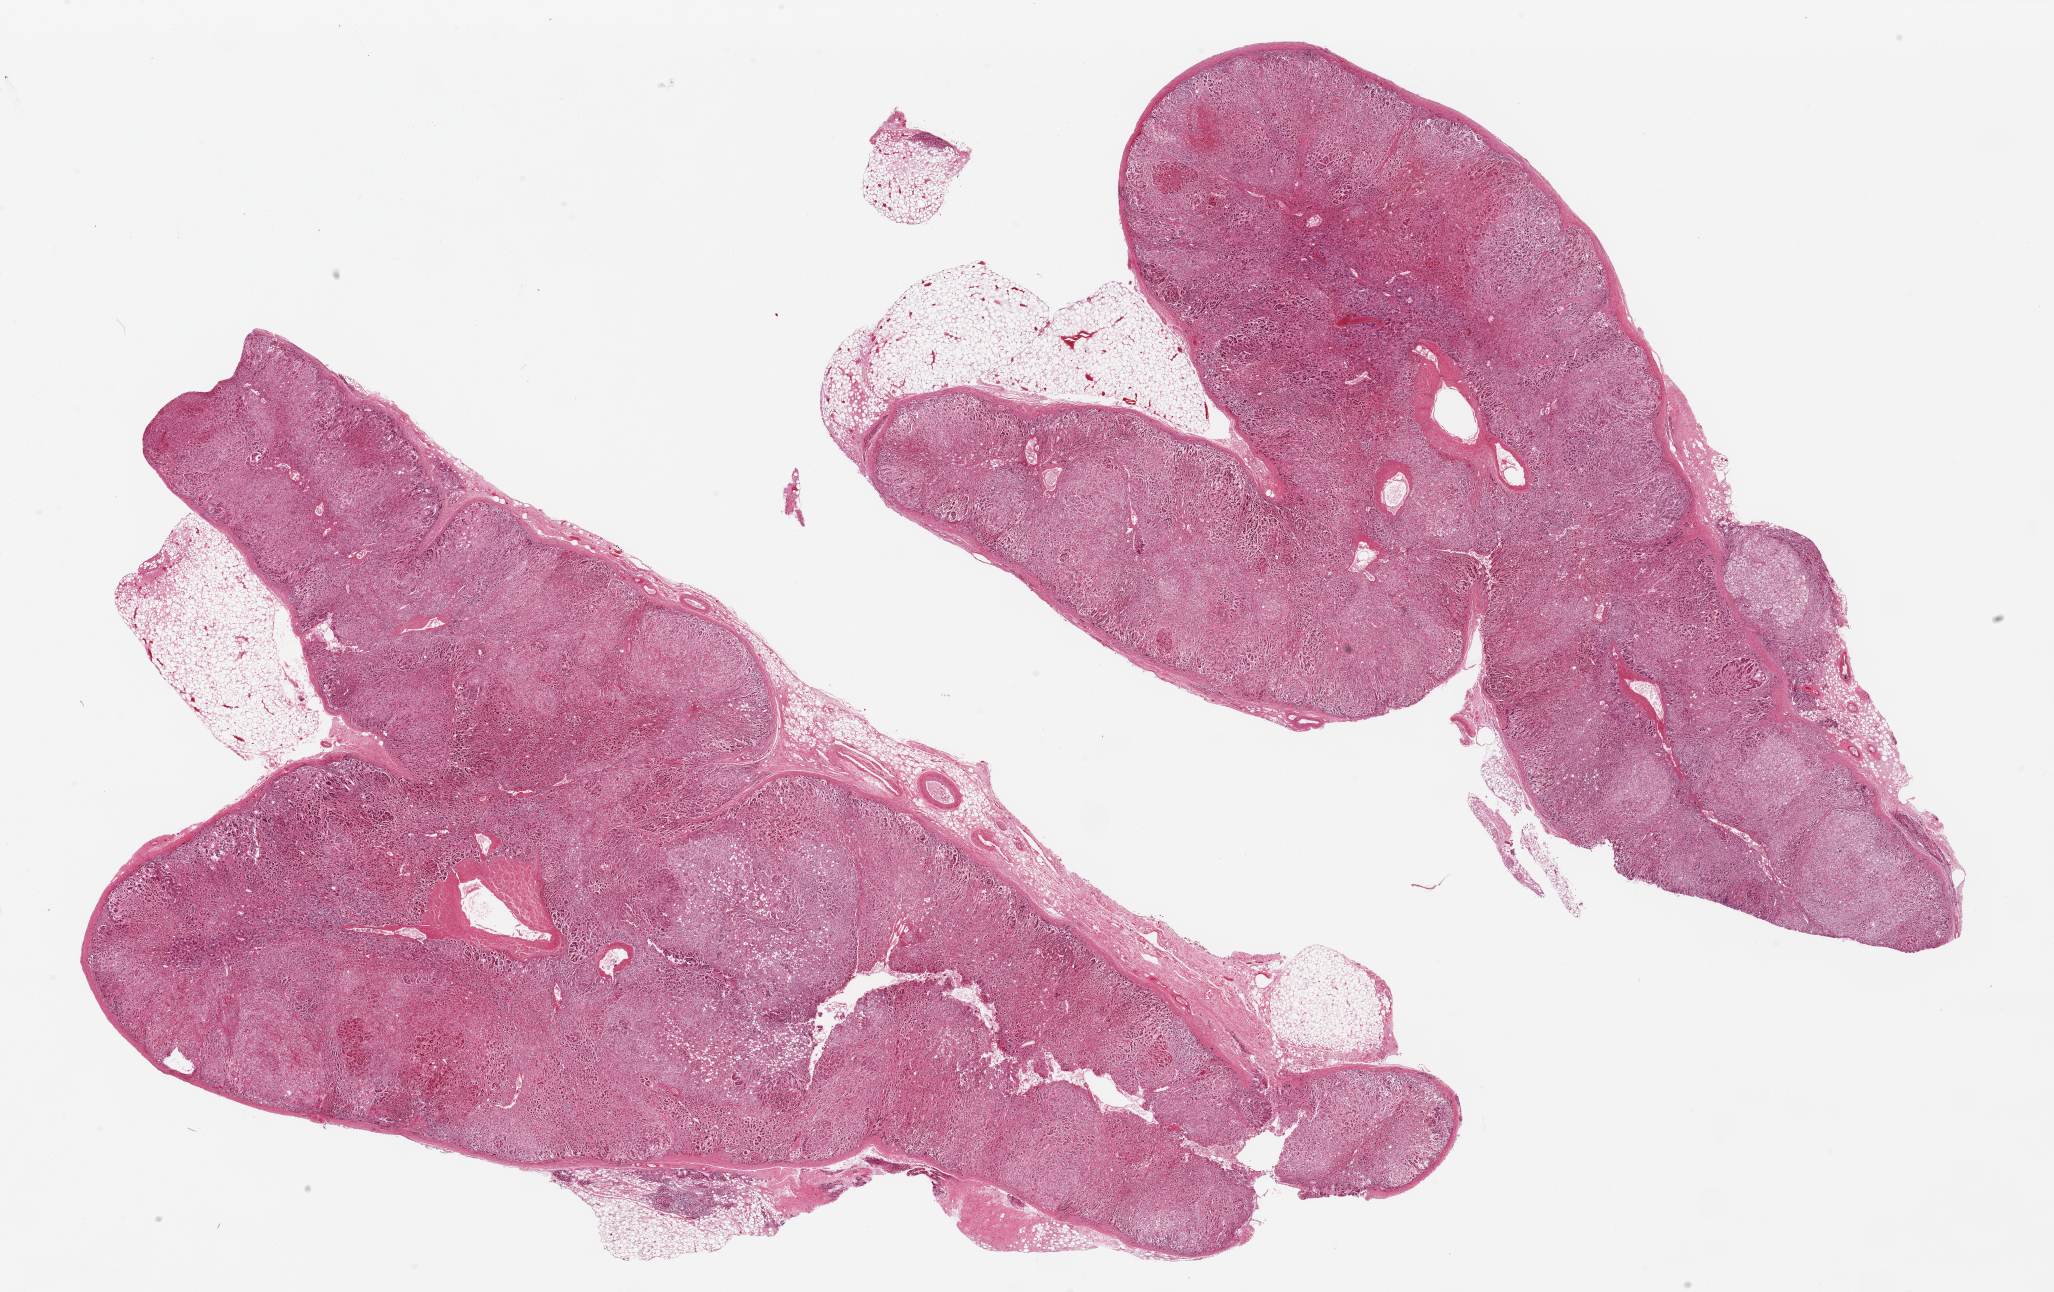
Whole-slide image, H&E stain, shown as a low-resolution overview of the whole scanned area (about 32.5 x 20.4 mm, slide scanned at 20x); PAXgene-fixed paraffin-embedded (PFPE) section; target tissue: adrenal gland; tissue donor sample.
* review note (as recorded): 2 ~20x10mm aliquots, all cortex, moderately-severely autolyzed